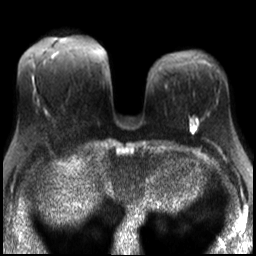
Breast MRI, one axial slice; position 12 of 30 along the scan axis; diffusion-weighted series; image 2 of 4 stored at this slice position (different b-values; order by instance number); 3 T; 4 mm slice thickness; 256 × 256 image matrix, field of view 320 × 320 mm. Female patient.
Structures marked on this image (expert manual segmentation):
- tumour on diffusion-weighted imaging: bounding box <191,122,196,129> (left, top, right, bottom; pixels)